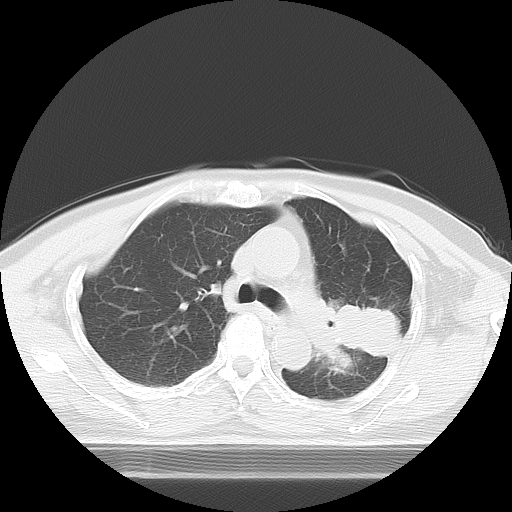
Chest CT, one axial slice. Slice 4 of 21 in the series (ordered by position). Lung window (W 1500 / L -600 HU). 5 mm slice thickness. 512 × 512 image matrix, field of view 350 × 350 mm. Female patient, age 74 years. Case-level facts recorded for this patient, not image findings: clinical TNM (as recorded): T3 N1 M1c; histopathological grade: G3.
Annotated regions visible in this slice (rectangle marked by the reading radiologist):
- lung tumour (recorded histology: small cell carcinoma): bounding box (x1, y1, x2, y2) in pixels: (311, 295, 403, 379)